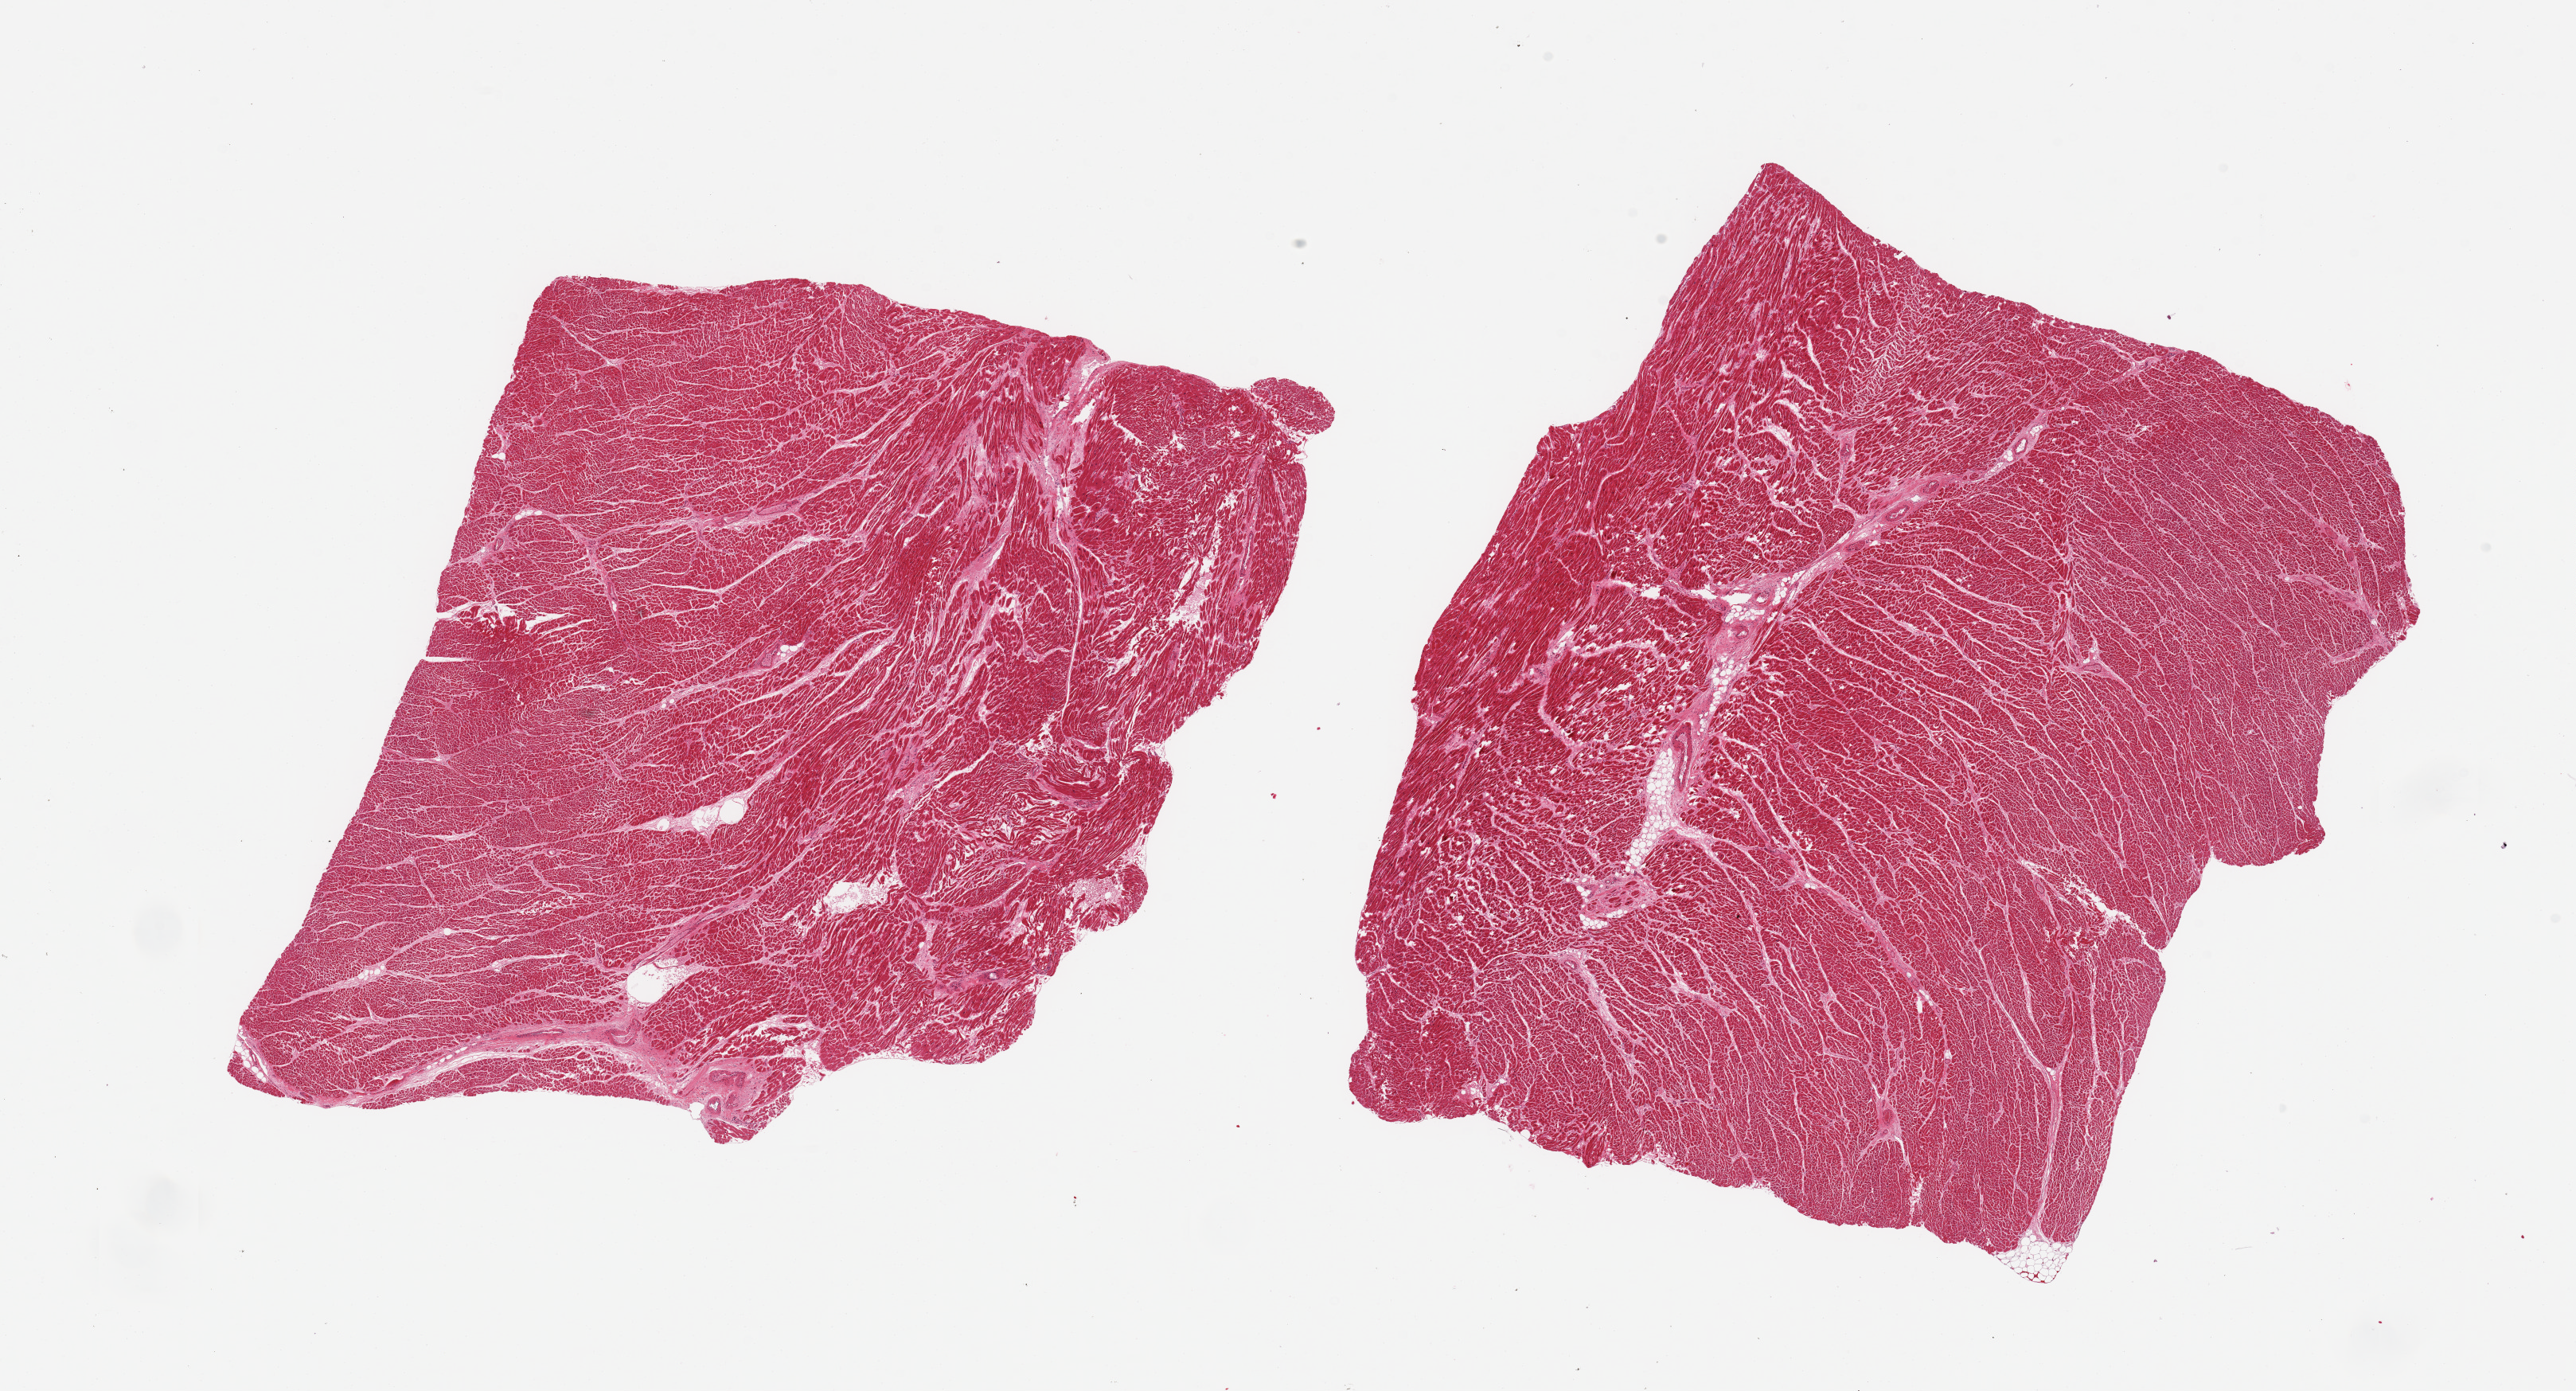
Digitized H&E-stained section, whole scanned area (about 25.6 x 13.8 mm) shown as a low-resolution overview, PAXgene-fixed paraffin-embedded (PFPE) section, section of heart (target tissue), donor tissue sample.
* review note (as recorded): 2 pieces, moderate-marked chronic ischemic damage/interstitial fibrosis